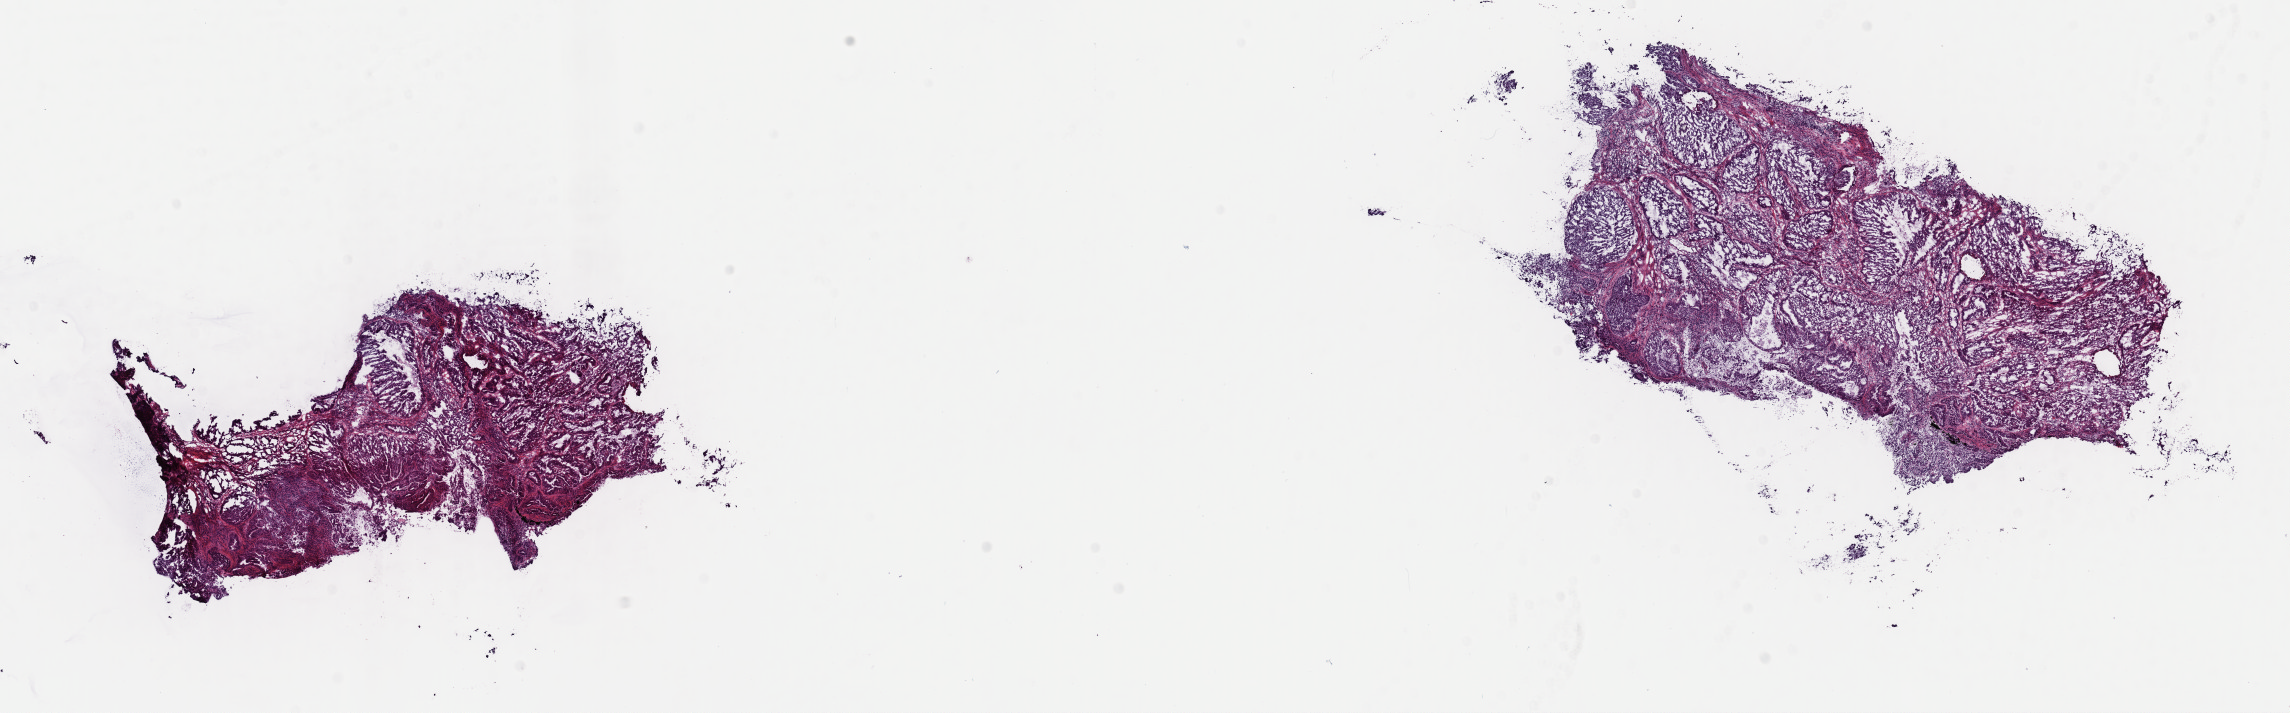
H&E whole-slide image, low-resolution overview of the scanned area, about 18.1 x 5.6 mm (from a 40x scan); frozen section from the top of the tissue portion; primary tumour sample from the uterus. Female, age 73 years at initial diagnosis. Histologic grade: G3 (poorly differentiated). Composition of this section per pathologist review: tumour cells 92%, tumour nuclei 85%, normal cells 5%, stromal cells 0%, necrosis 3%. Infiltration values recorded for this section: lymphocyte infiltration 3%, monocyte infiltration 0%, neutrophil infiltration 1%.
* lymph nodes positive (case pathology): 0 of 21 examined
* FIGO stage: IA
* histologic diagnosis: Serous cystadenocarcinoma, NOS (endometrium)